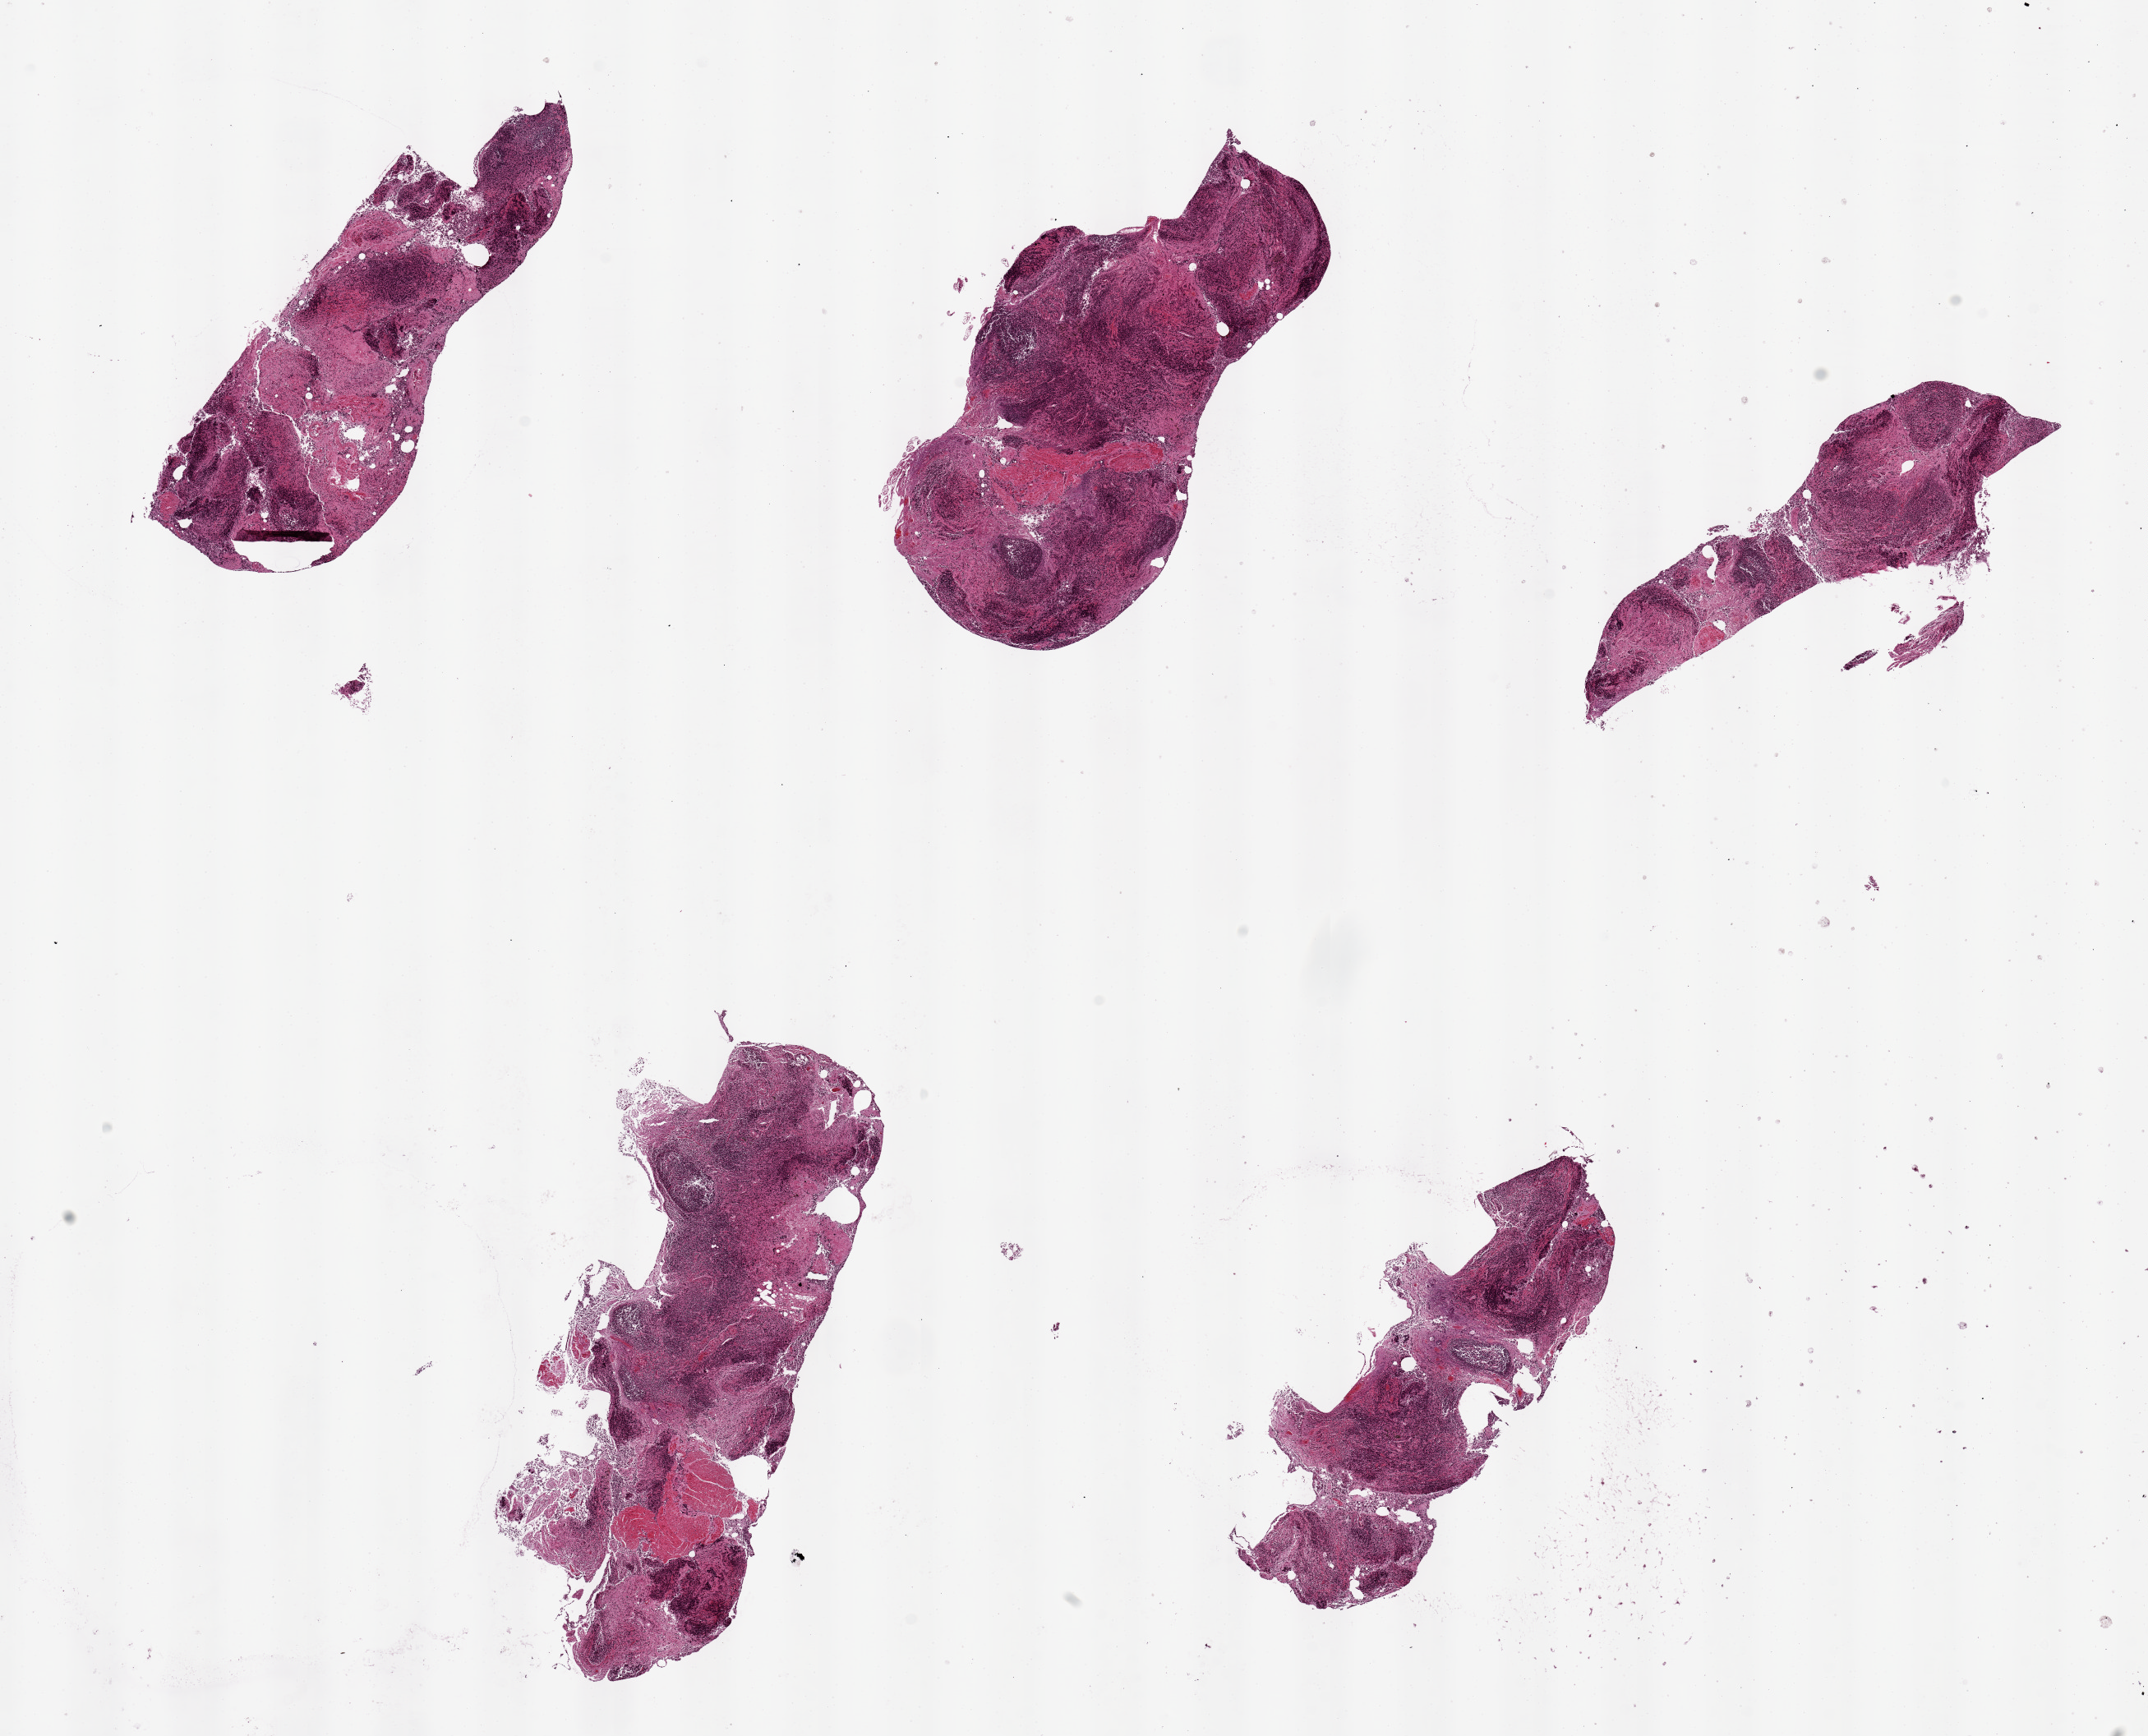
Digitized hematoxylin and eosin (H&E)-stained section — shown as a low-resolution overview of the whole scanned area (about 20.7 x 16.7 mm); PAXgene-fixed paraffin-embedded (PFPE) section; sampled site (target tissue): ileum; tissue donor sample. Male donor.
Reviewer comment on this tissue sample: 5 pieces, up to 7x3mm; mucosa autolyzed, abundant lymphoid elements, ~50-60% of specimens.